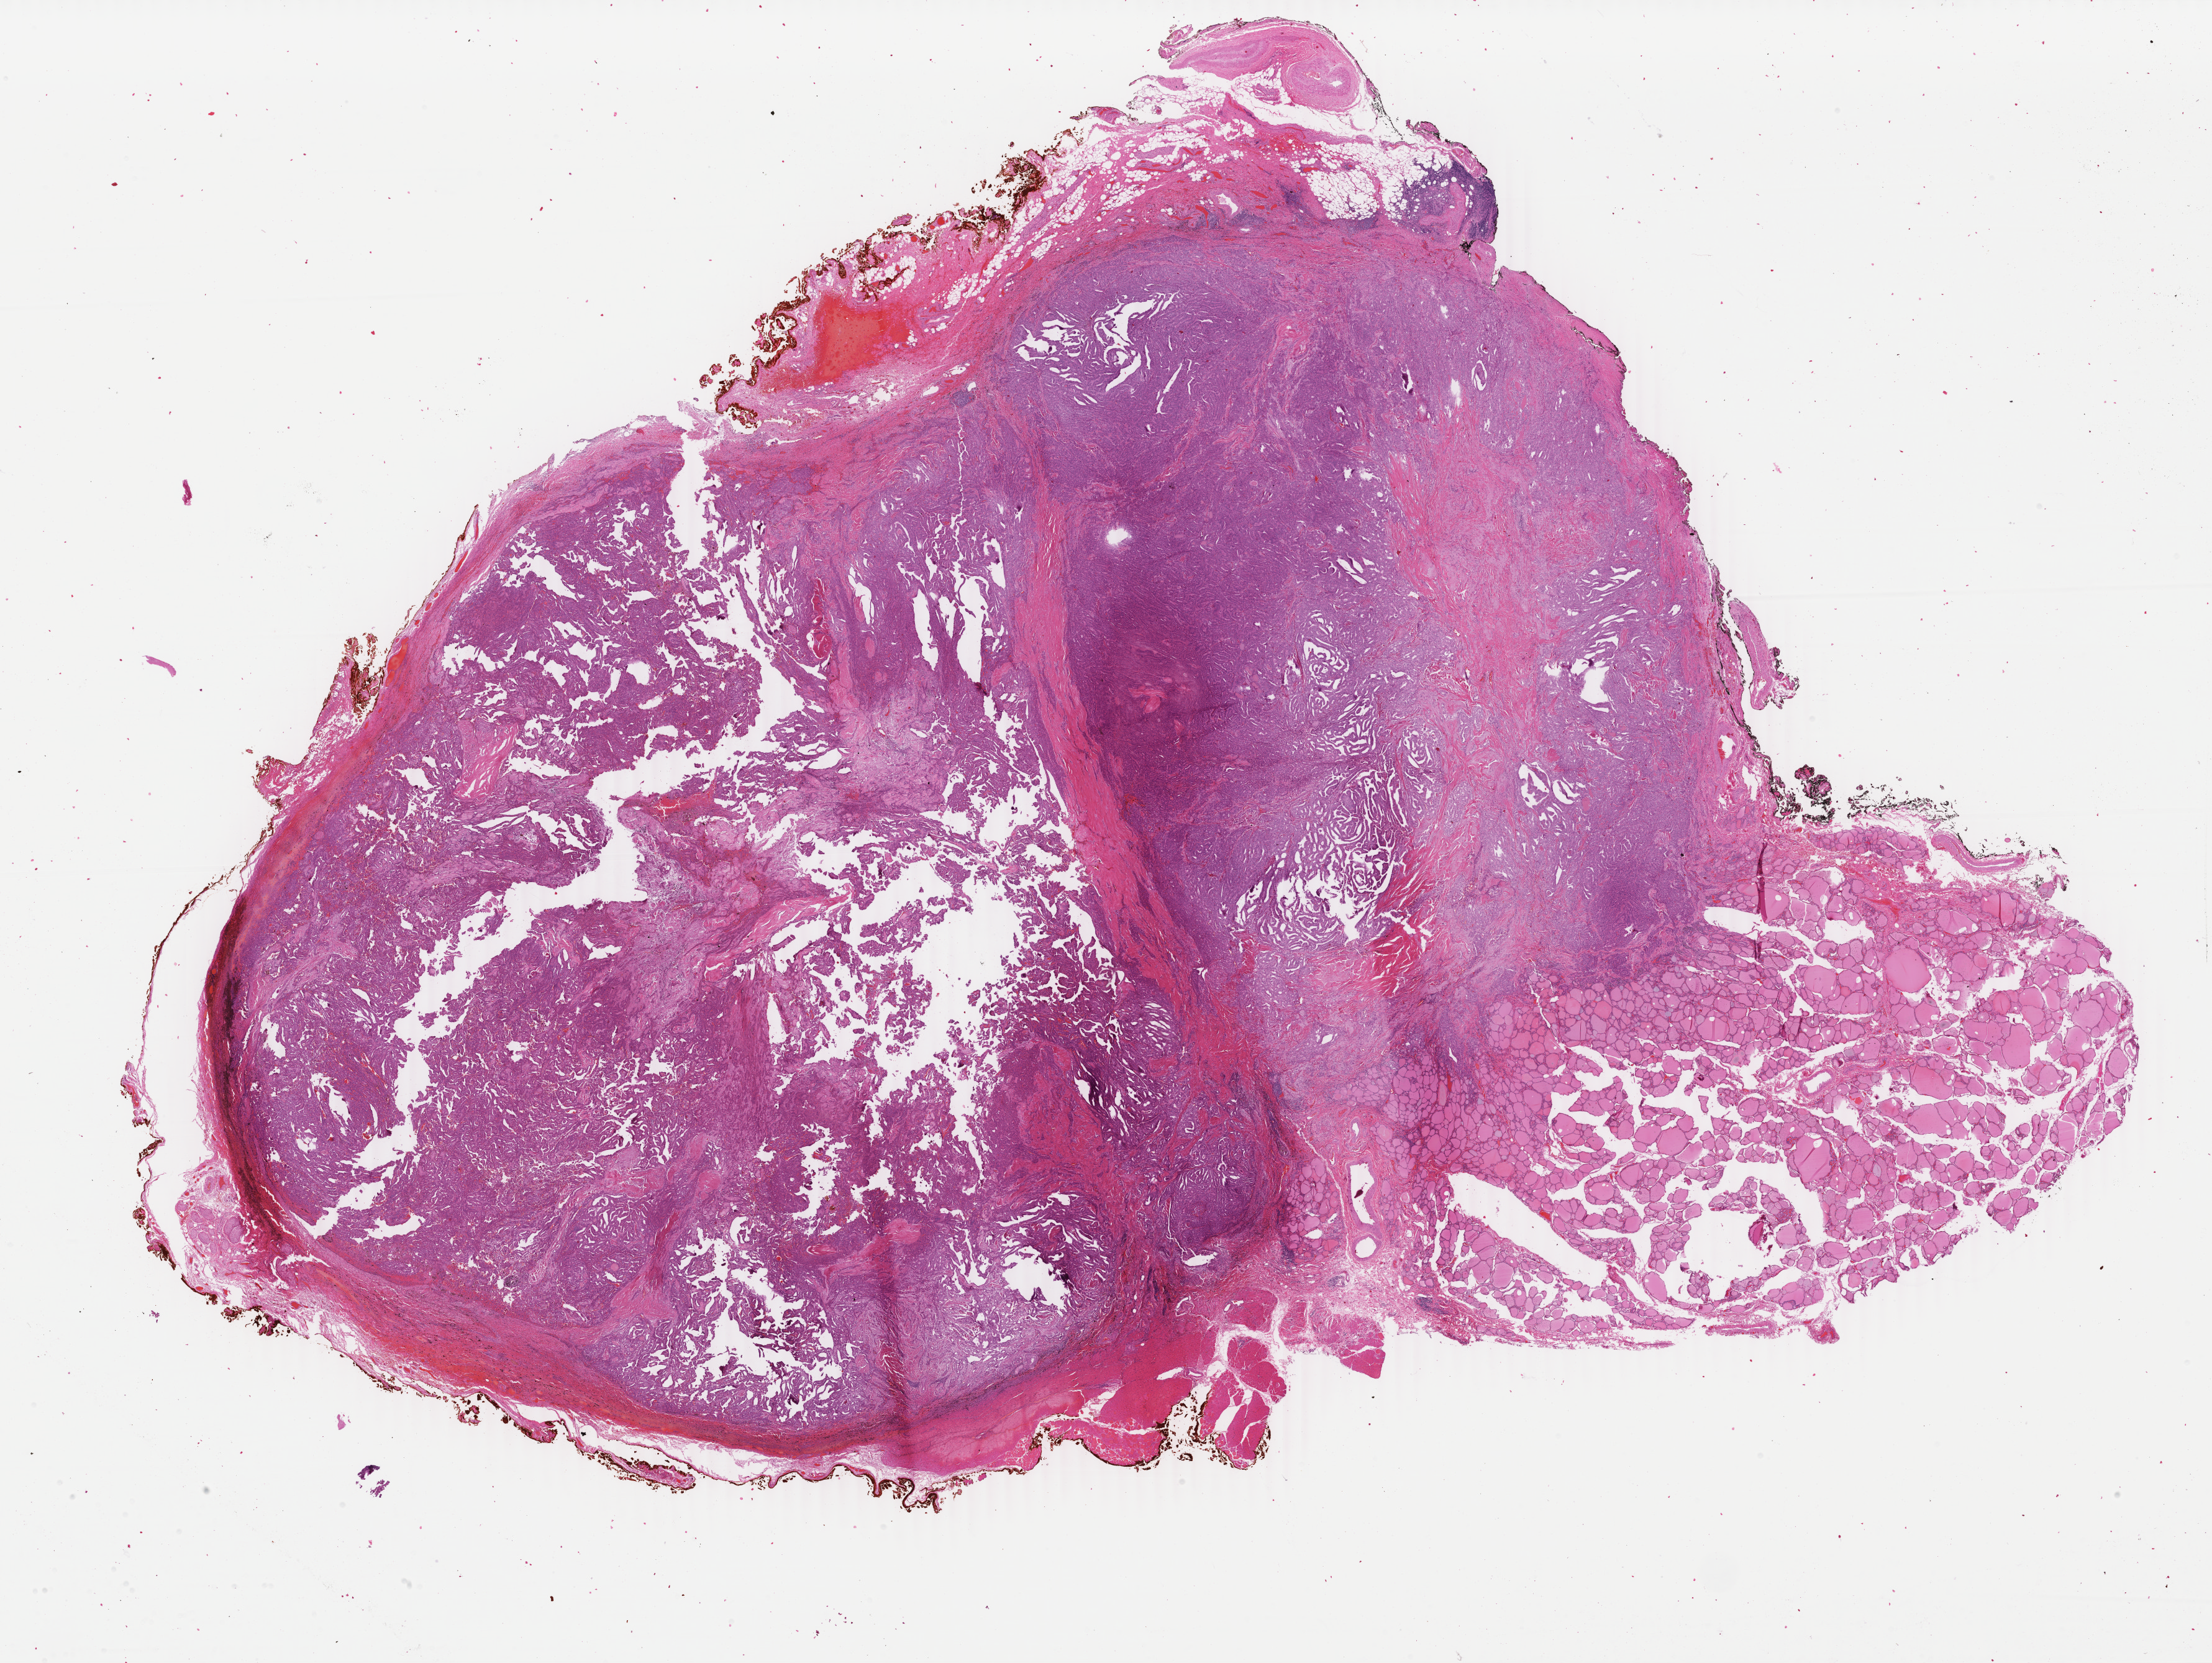
Whole-slide histology image, Hematoxylin and eosin (H&E) stained — low-resolution overview of the scanned area, about 28.3 x 21.3 mm; formalin-fixed paraffin-embedded (FFPE) diagnostic section; primary tumour sample from the thyroid. Female, age 52 years at initial diagnosis.
* histologic diagnosis: Papillary carcinoma, columnar cell (thyroid gland)
* laterality: left
* AJCC pathologic stage: IVA (7th edition)
* lymph nodes positive (case pathology): 2 of 12 examined